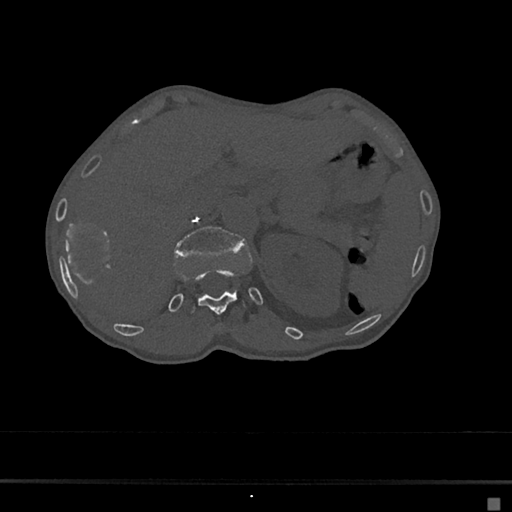
CT including the spine, one axial slice. Position 114 of 797 along the scan axis. Reconstruction kernel Br40s/3. Bone window (W 1800 / L 400 HU). 0.5 mm slice thickness. 512 × 512 image matrix. Female patient, age 68 years. Case-level facts recorded for this patient, not image findings: primary cancer: renal.
Outlined on this slice (semi-automatically segmented with operator editing):
- L1 vertebra: bounding box <173,226,247,256> (left, top, right, bottom; pixels)
- T11 vertebra: <217,331,222,335>
- T12 vertebra: <190,267,246,315>